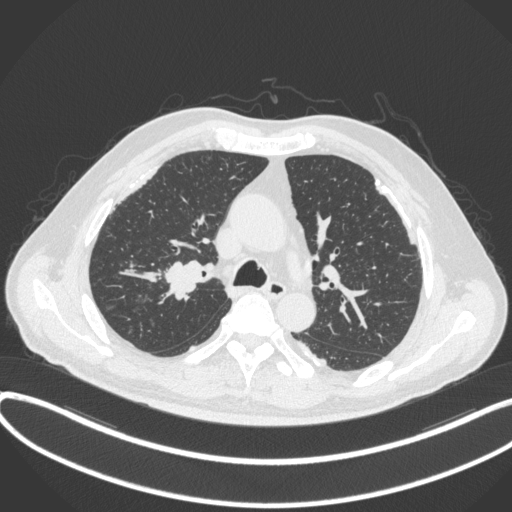
Chest CT, one axial slice. Position 286 of 455 along the scan axis. 120 kVp. Lung window (W 1500 / L -600 HU). 512 × 512 image matrix. Male patient, age 58 years. From the clinical record (not read from this slice): clinical TNM (as recorded): T1c N0 M0.
Annotated regions visible in this slice (bounding box drawn by a radiologist):
- lung tumour (recorded histology: squamous cell carcinoma): bounding box [x1, y1, x2, y2] px = [161, 259, 206, 300]